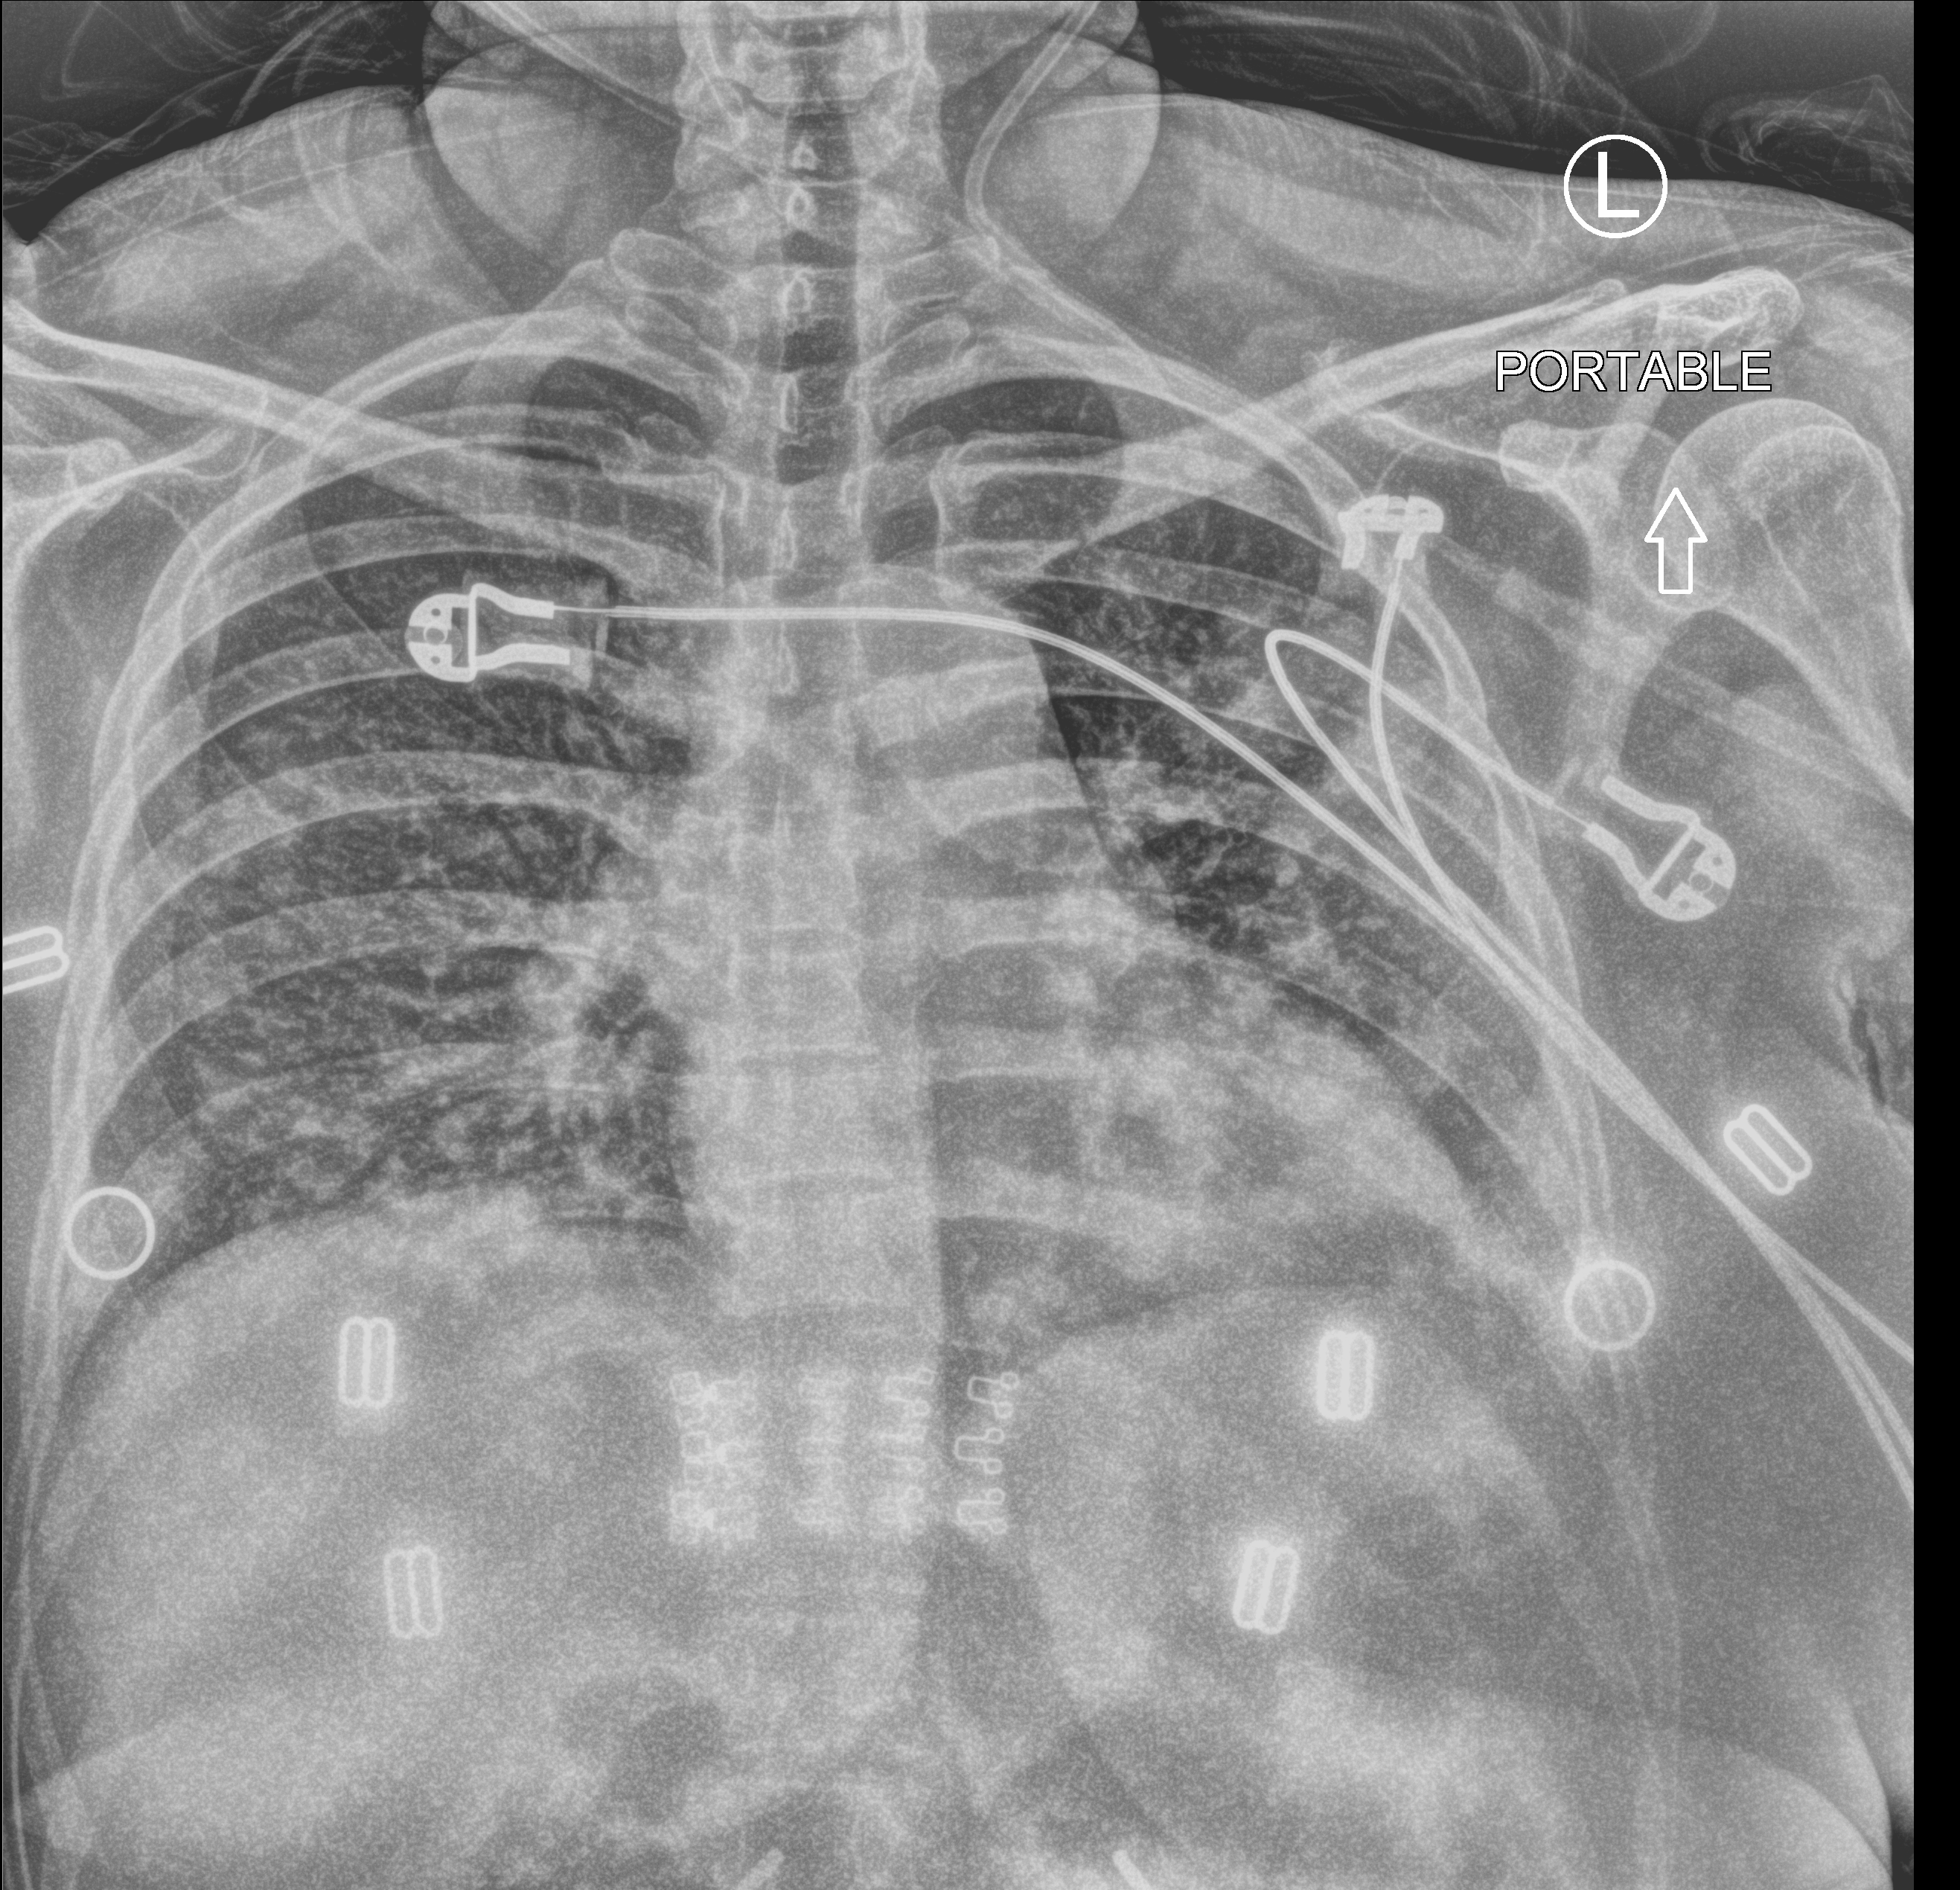
Chest X-ray (portable), anteroposterior (AP) projection. Female patient hospitalised with COVID-19, age 18–59 years.
Hospital-stay facts (about this admission, not read from this image; timing relative to this image not recorded): mechanically ventilated during this hospital stay: no.